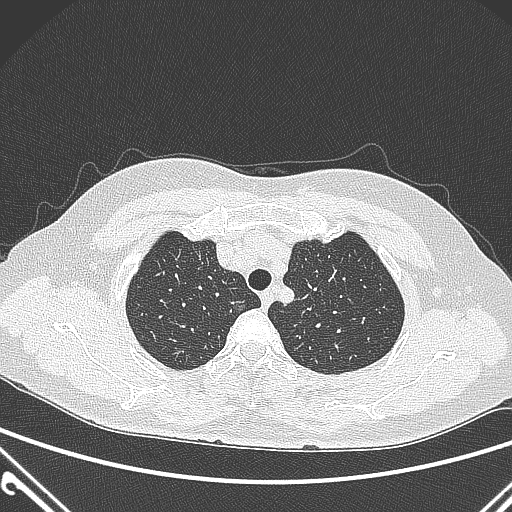
Chest CT, one axial slice. Position 234 of 300 along the scan axis. 120 kVp. Lung window (W 1500 / L -600 HU). 1 mm slice thickness. 512 × 512 image matrix, field of view 350 × 350 mm. Female patient, age 54 years. Case-level facts recorded for this patient, not image findings: clinical TNM (as recorded): T1a N0 M0; histopathological grade: G1.
Structures marked on this image (bounding box drawn by a radiologist):
- lung tumour (recorded histology: adenocarcinoma): box from (x=229, y=297) to (x=252, y=321) px